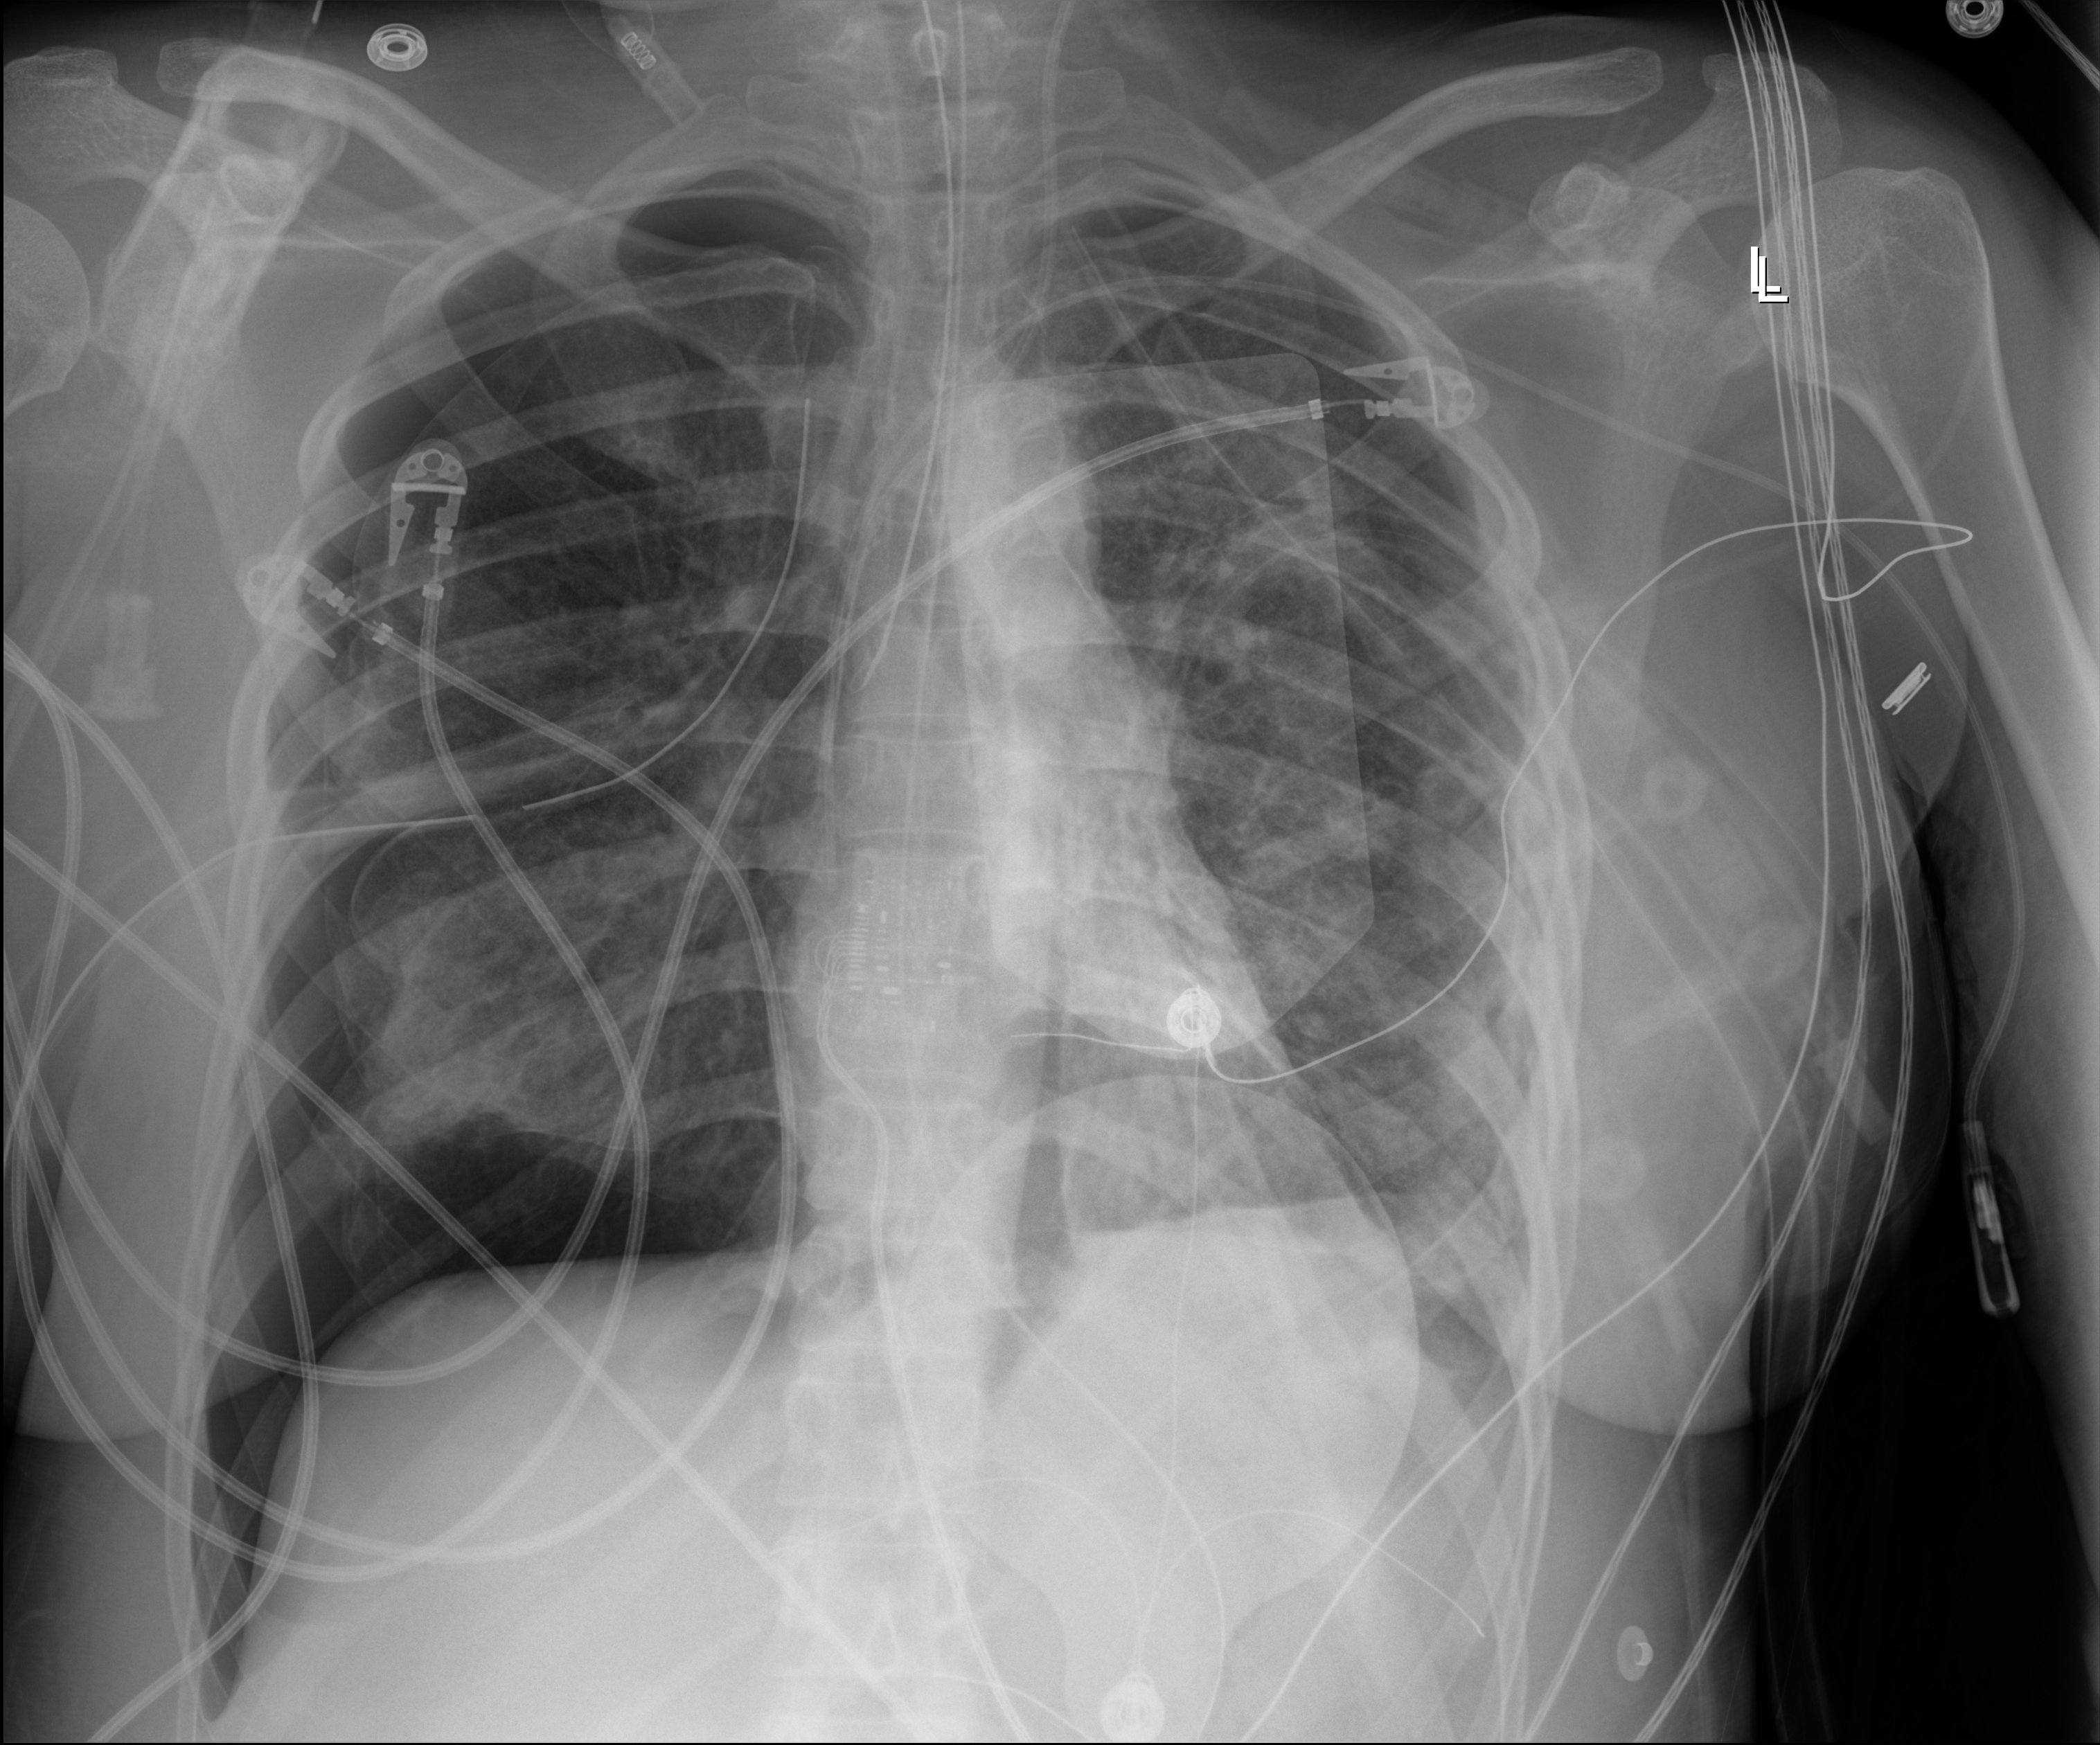
Bedside chest radiograph (digital radiography), anteroposterior (AP) projection. Patient hospitalised with COVID-19, aged 18–59 years.
Hospital-stay facts (about this admission, not read from this image; timing relative to this image not recorded): hypertension (admission record): no.